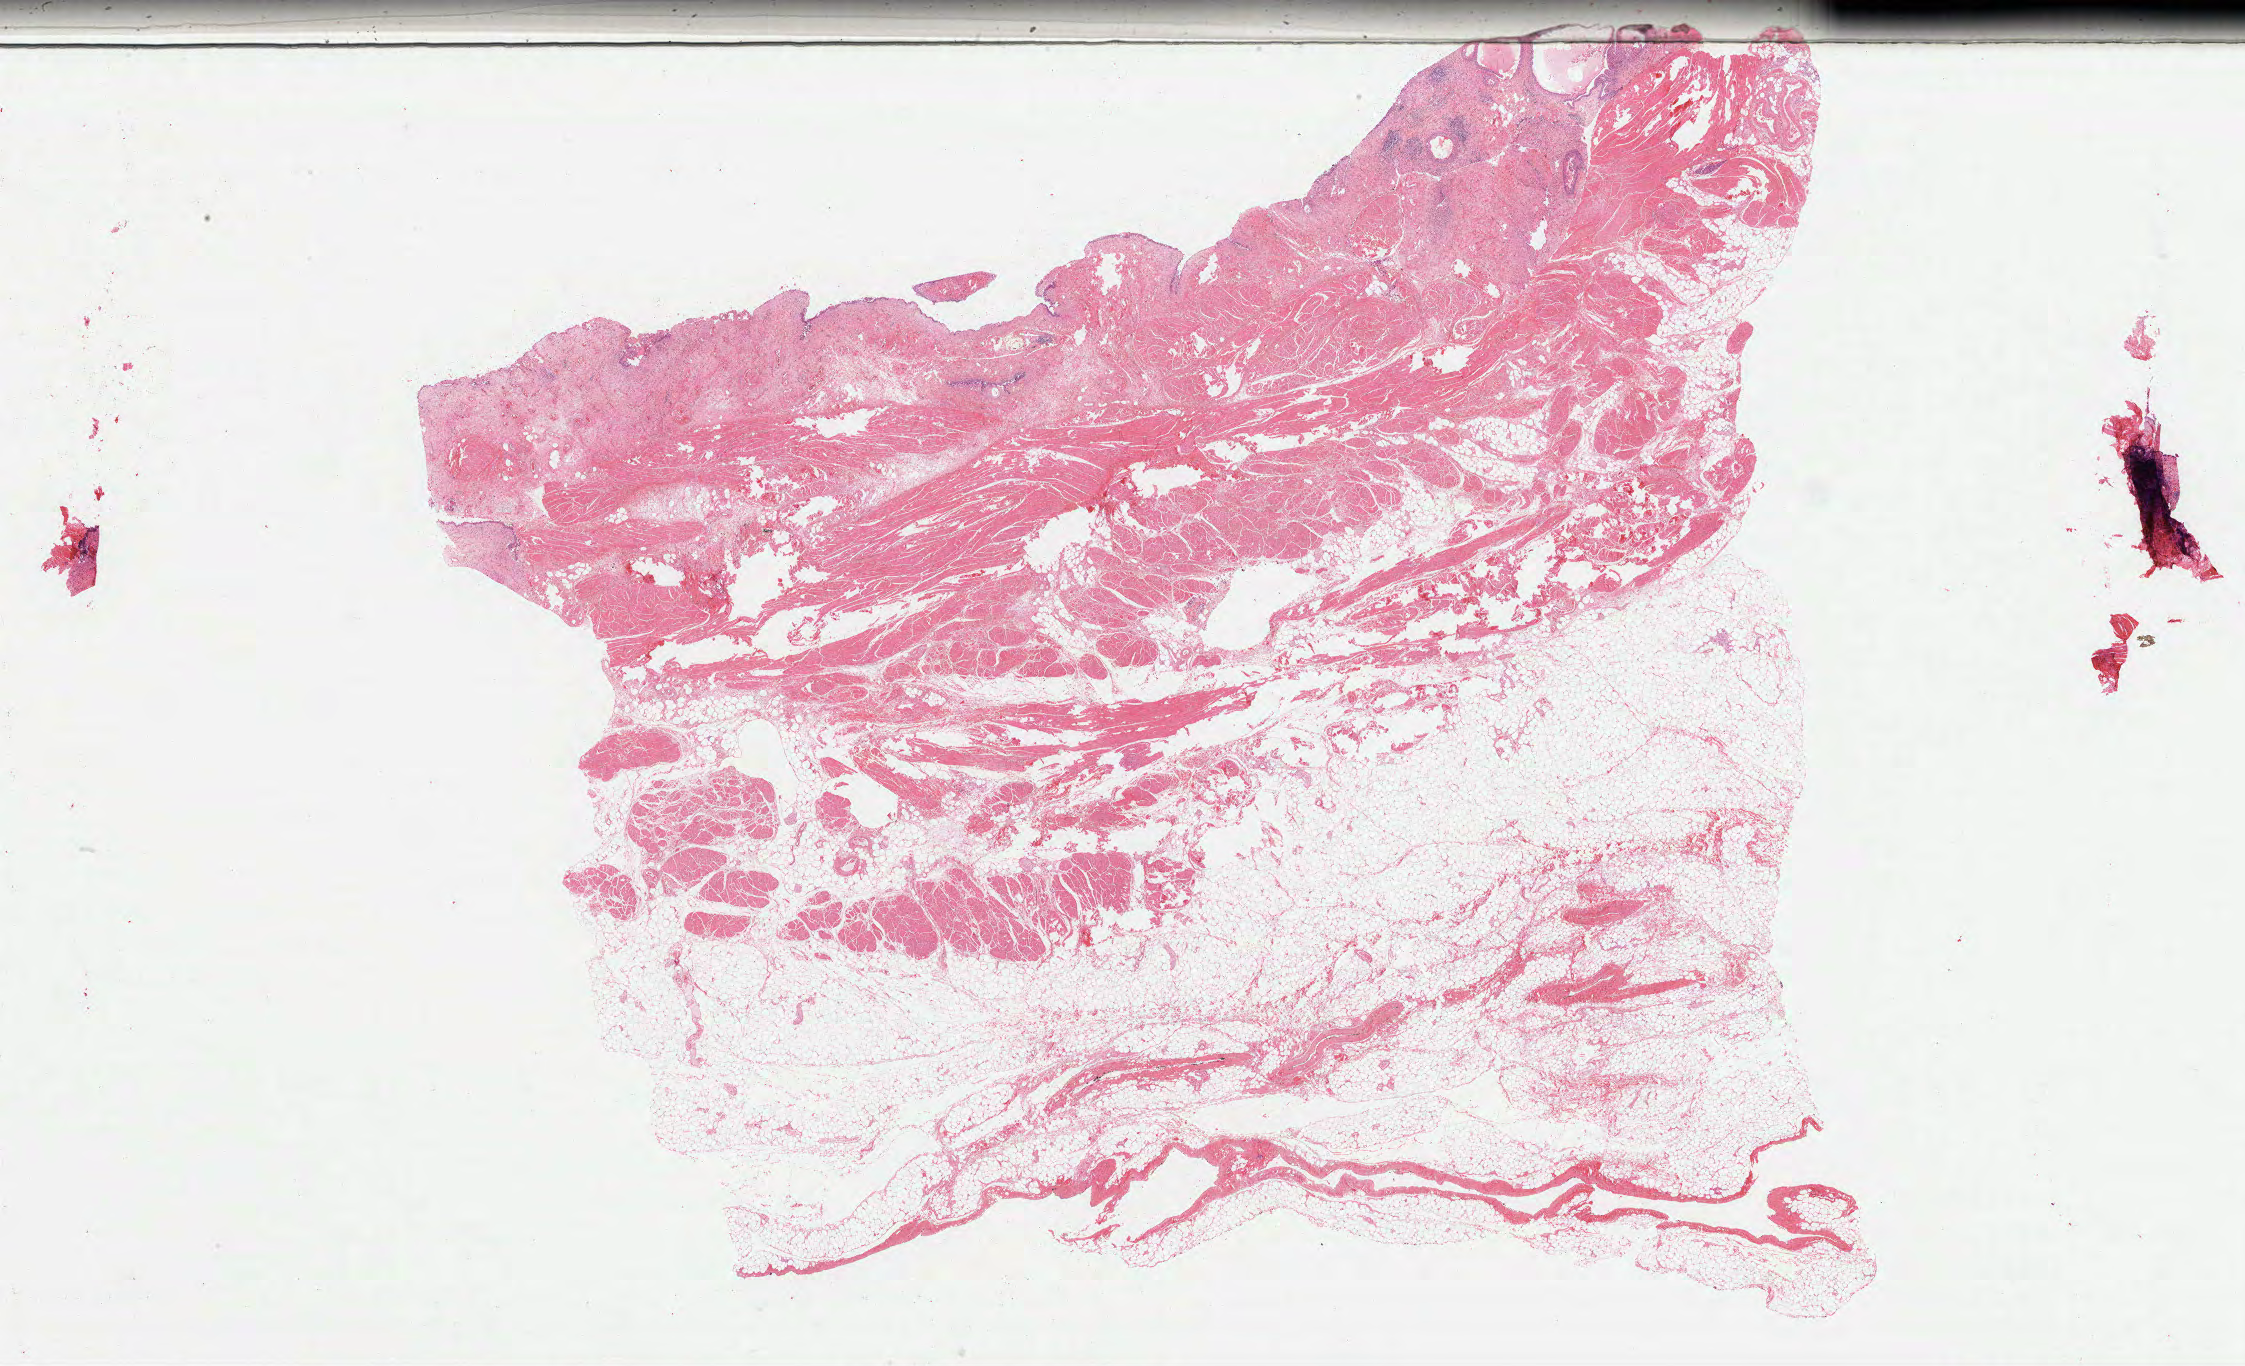
H&E whole-slide image, whole scanned area (about 35.6 x 21.7 mm) shown as a low-resolution overview; FFPE section; sample: primary tumour, bladder. Patient: male, age at initial diagnosis 77 years. Histologic grade: high grade.
• AJCC pathologic stage: II (7th edition)
• histologic diagnosis: Transitional cell carcinoma